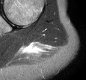
MRI of an extremity soft-tissue mass, one axial slice; slice 20 of 30 in the series (ordered by position); STIR; MR volume resampled by the dataset authors to the PET/CT grid (not the native acquisition matrix); 86 × 80 image matrix, field of view 84 × 78 mm. Female patient. From the clinical record (not read from this slice): histological type: malignant fibrous histiocytoma; grade: low; site of the primary tumour: left arm.
Structures marked on this image (expert contour drawn on MRI and transferred to this co-registered scan by the dataset authors):
- gross tumour volume (mass): bounding box [x1, y1, x2, y2] px = [22, 42, 39, 52]